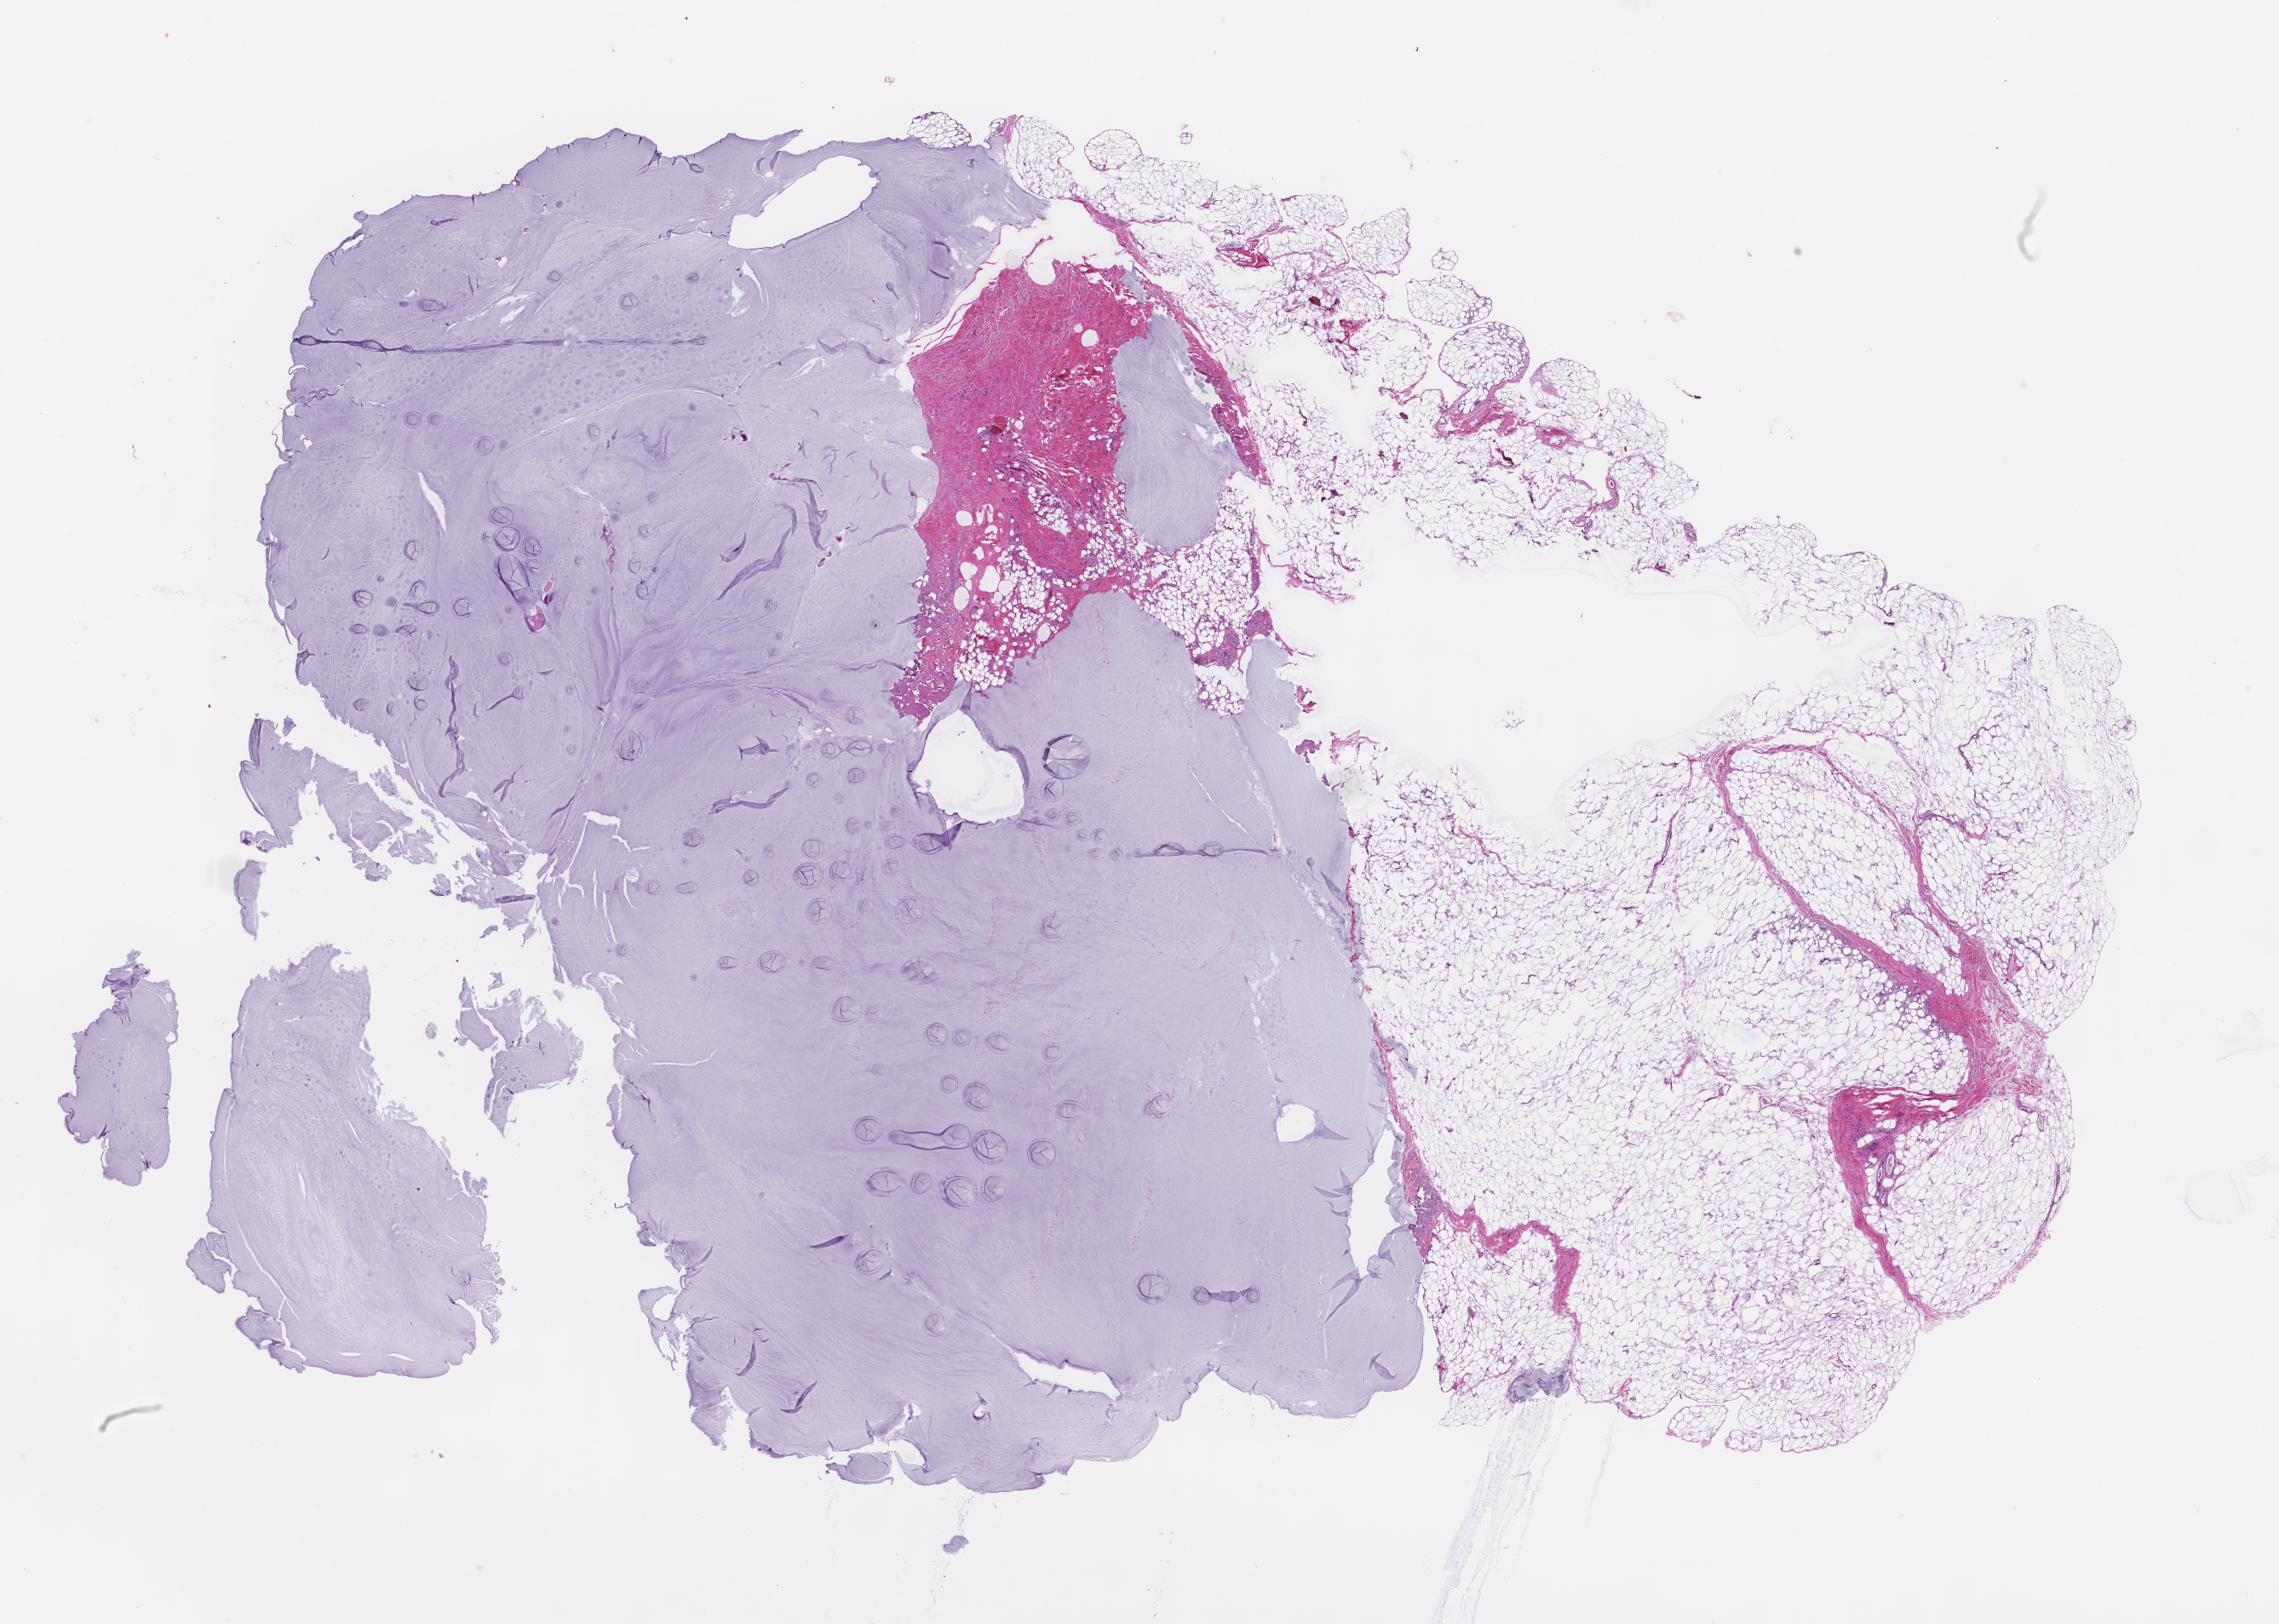
Hematoxylin and eosin (H&E) whole-slide image — whole scanned area (about 21.6 x 15.4 mm) shown as a low-resolution overview, formalin-fixed, paraffin-embedded (FFPE) tissue, specimen time point: collected at baseline (before treatment). Male patient.
This section: metastasis (sampled organ not recorded). Patient diagnosis (primary): Colorectal Carcinoma.